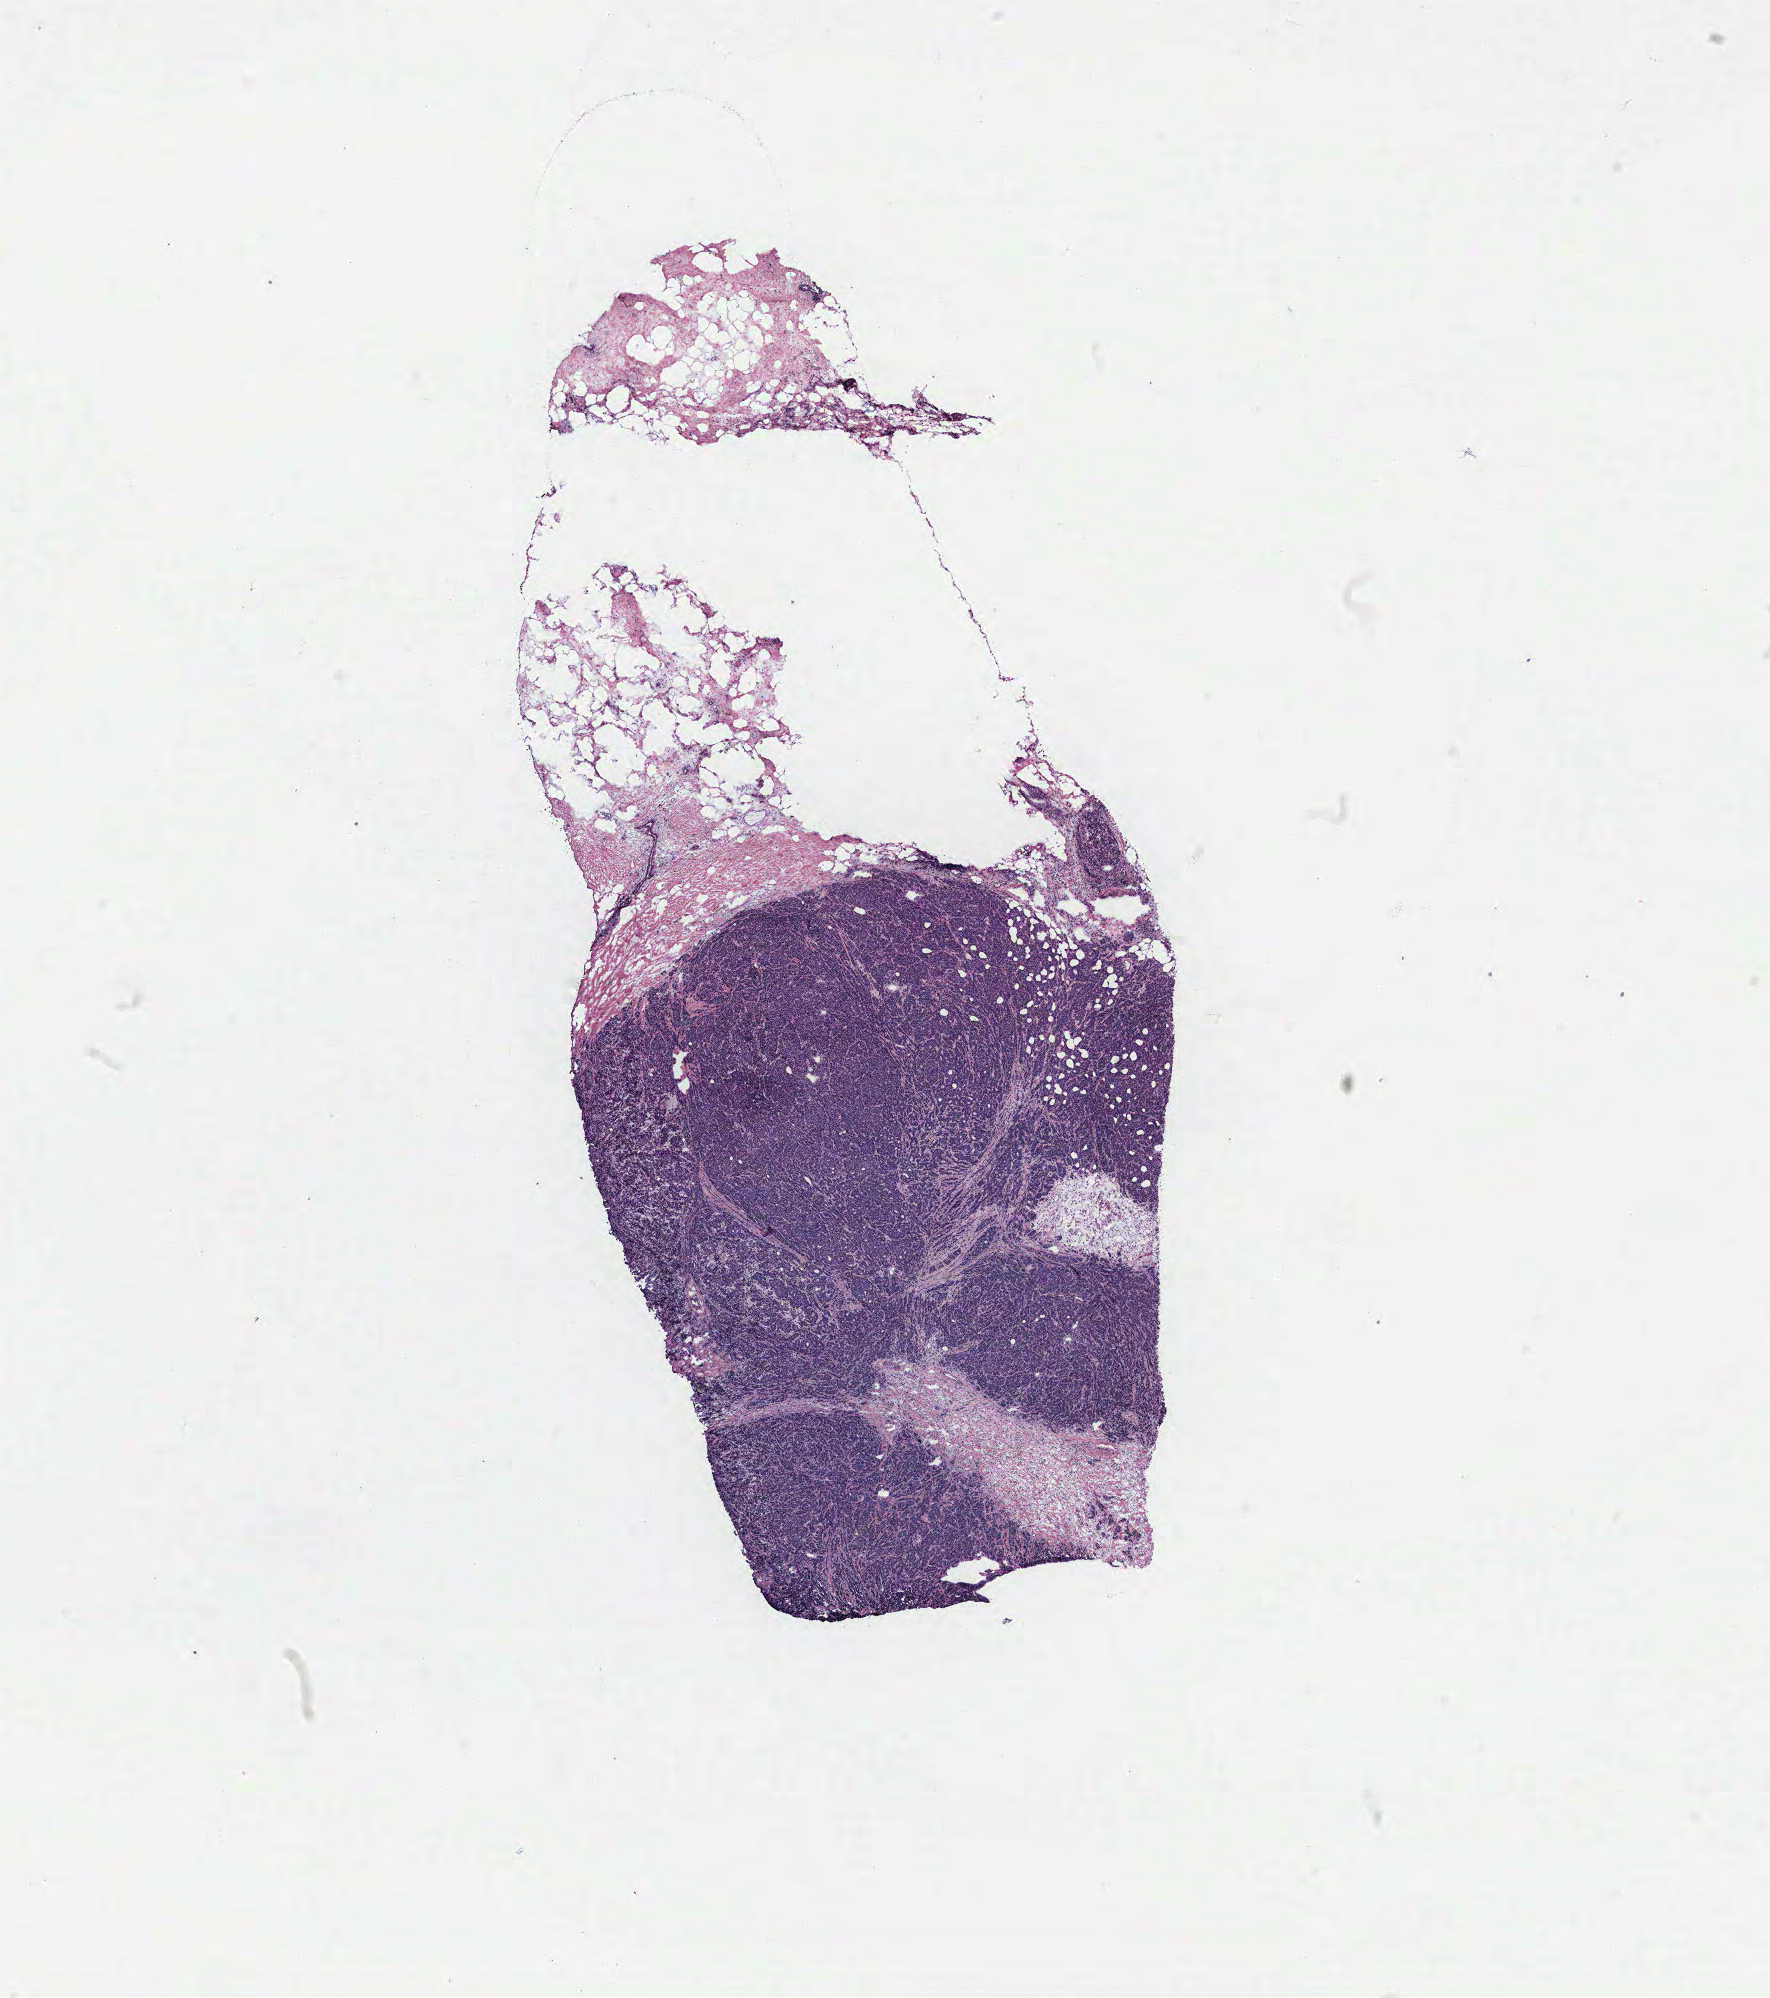
H&E-stained whole-slide image, low-resolution overview of the scanned area, about 14.2 x 16.0 mm (acquisition: 40x scan). Breast, tissue type not recorded. Patient: female, age 78 years.
* patient diagnosis: Infiltrating duct carcinoma, NOS